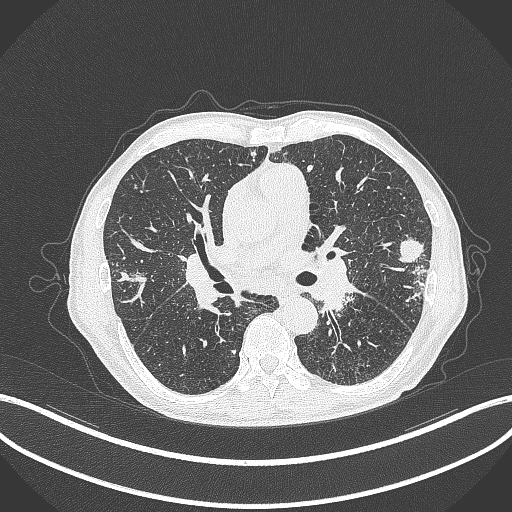
Chest CT, one axial slice. Slice 222 of 463 in the series (ordered by position). Reconstruction kernel B70f. Lung window (W 1500 / L -600 HU). 1 mm slice thickness. 512 × 512 image matrix, field of view 400 × 400 mm. Male patient, age 74 years. Case-level facts recorded for this patient, not image findings: clinical TNM (as recorded): T2a N1 M0.
Outlined on this slice (bounding box drawn by a radiologist):
- lung tumour (recorded histology: adenocarcinoma): bounding box <396,237,426,264> (left, top, right, bottom; pixels)